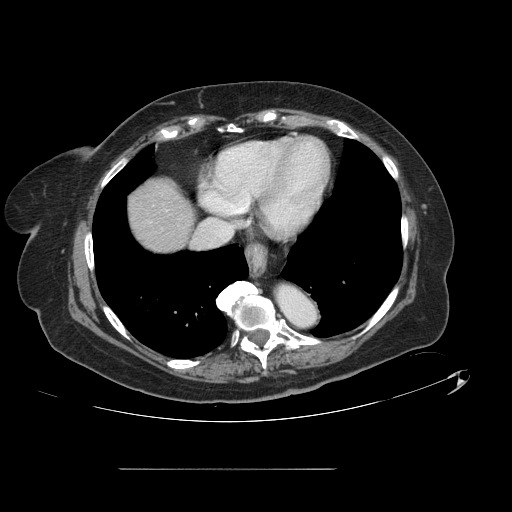
Contrast-enhanced abdominal CT, one axial slice; slice 126 of 148 in the series (ordered by position); intravenous contrast given; soft-tissue window (W 400 / L 40 HU); 2.5 mm slice thickness; 512 × 512 image matrix, field of view 439 × 439 mm. Female patient, age 75 years. From the clinical record (not read from this slice): diagnosis: colorectal cancer liver metastases, imaged before liver resection; multiple liver metastases: no; largest metastasis: 2.4 cm; chemotherapy before resection: no.
Outlined on this slice (manually delineated by an expert):
- liver: bounding box [x1, y1, x2, y2] px = [129, 179, 193, 251]
- planned liver remnant (the part of the liver to remain after resection): [129, 179, 193, 251]